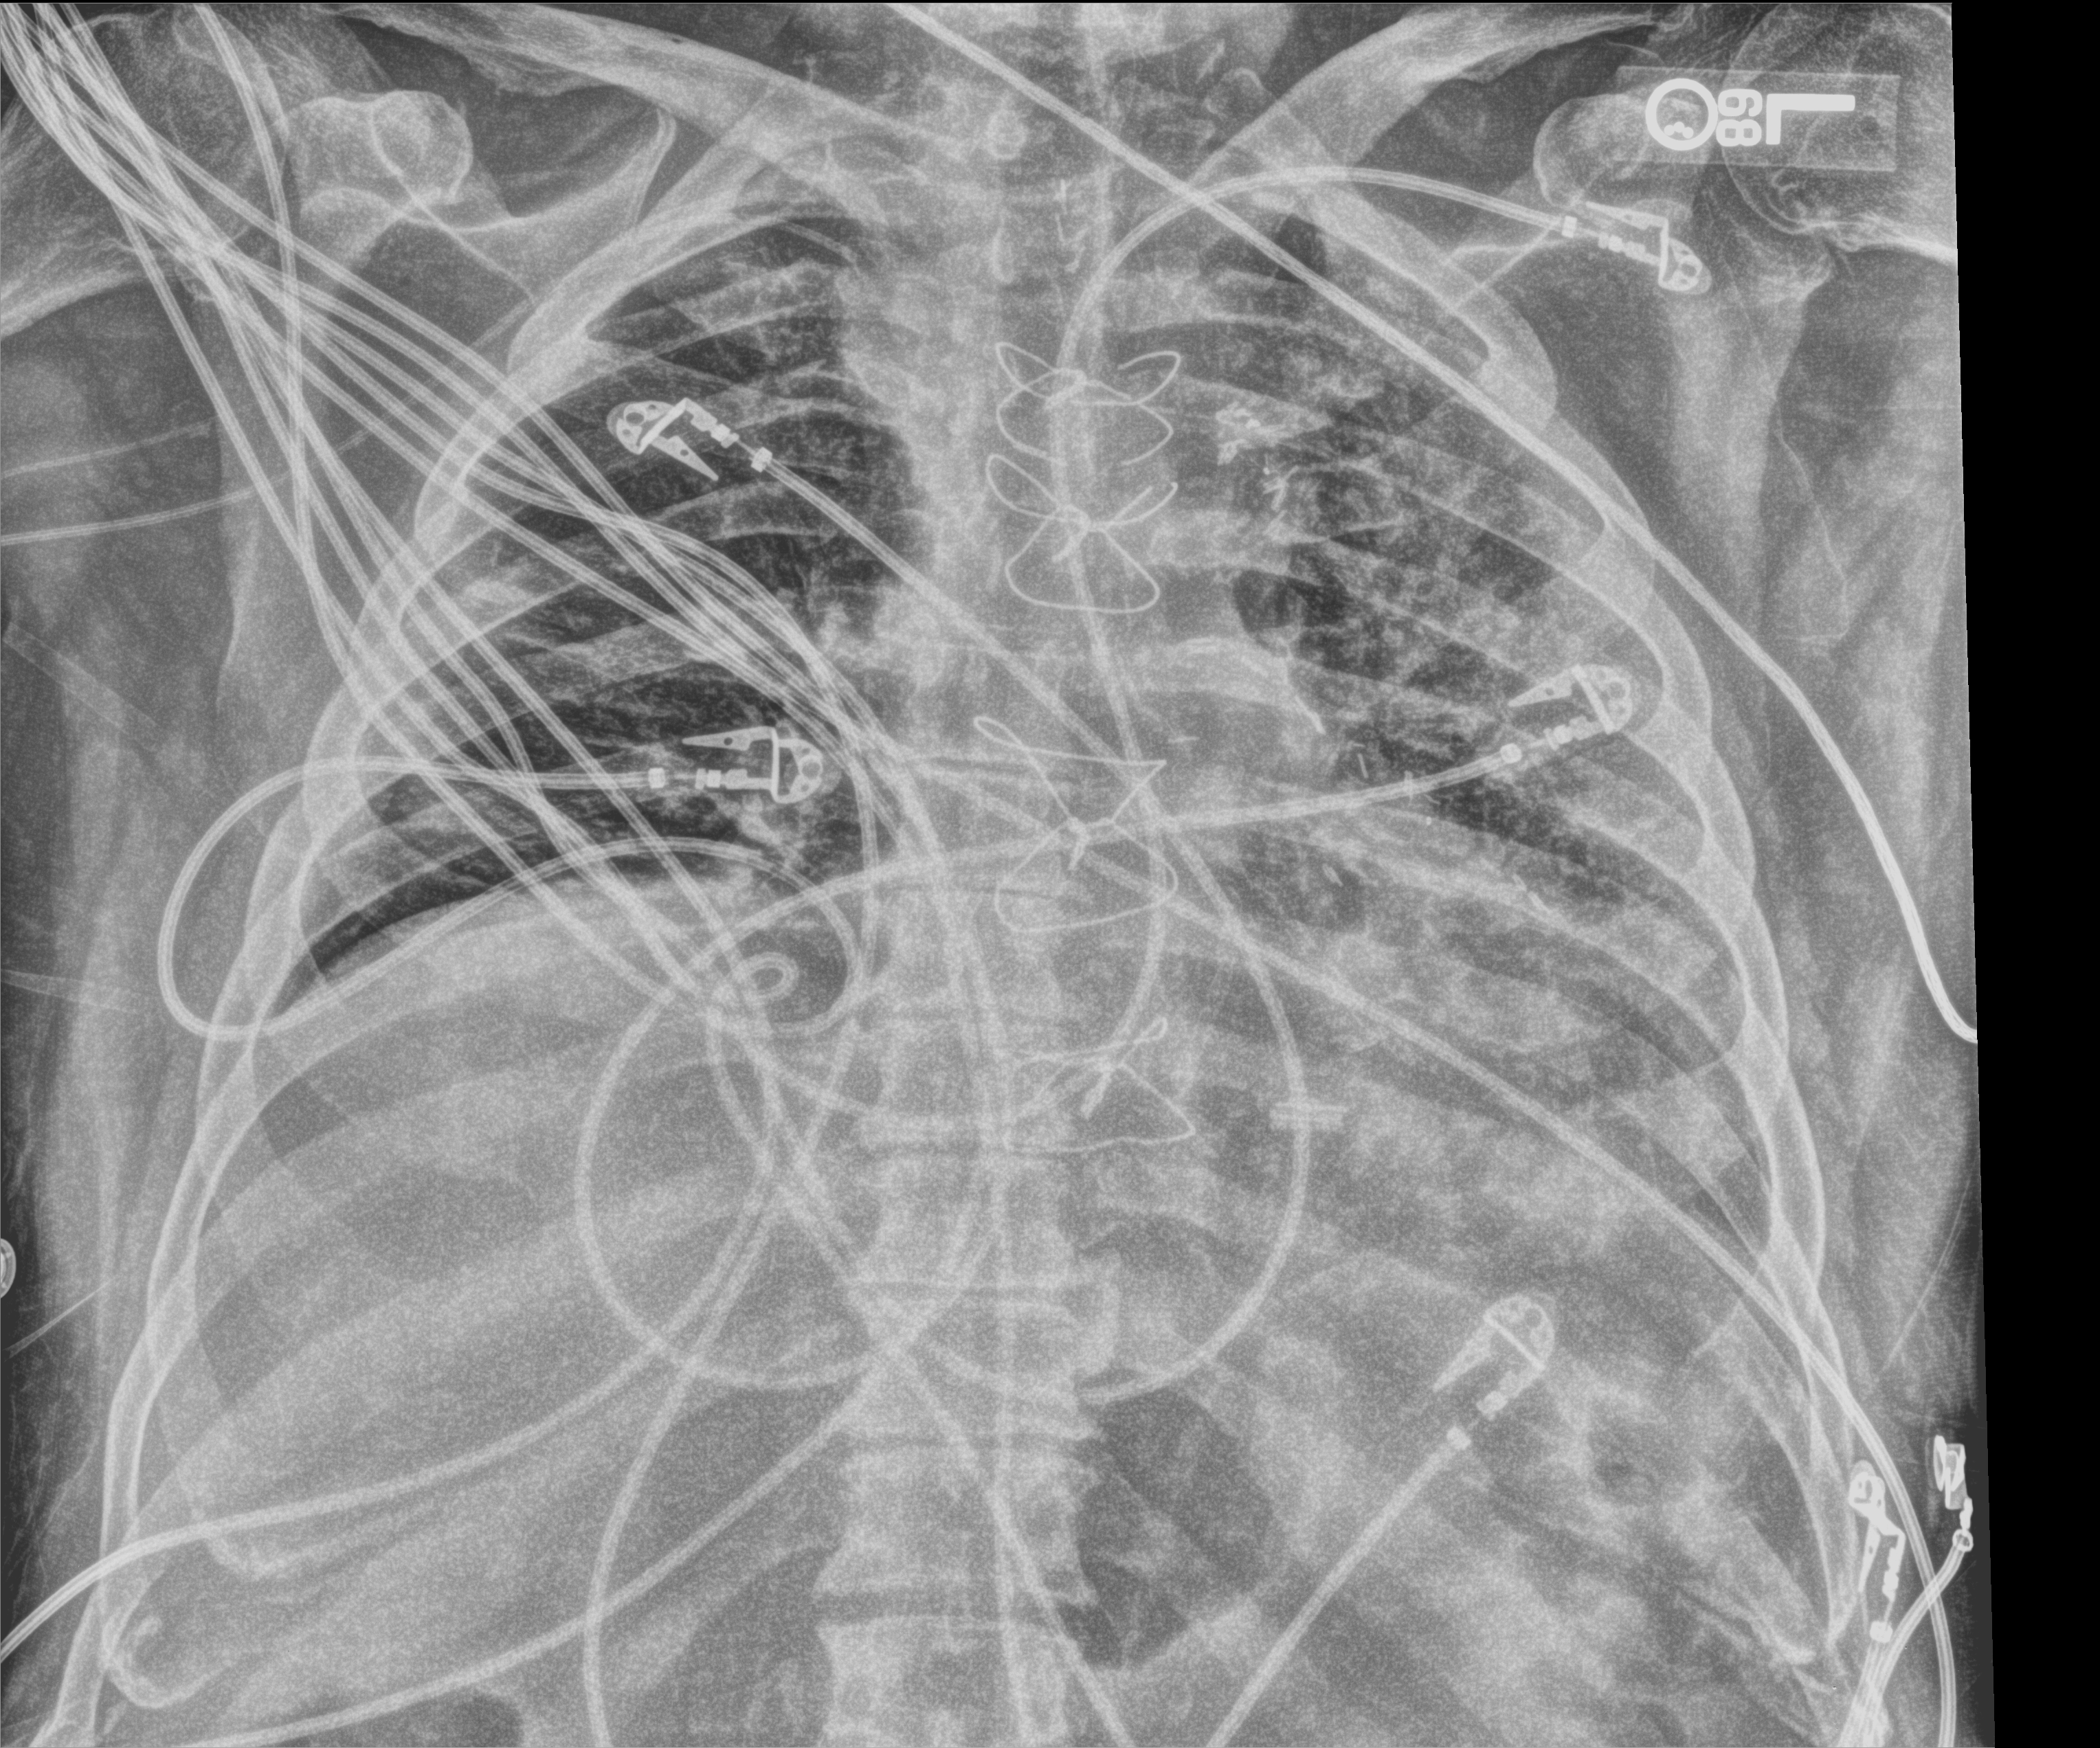
Bedside chest radiograph (computed radiography), anteroposterior (AP) projection. Male patient hospitalised with COVID-19, age 60–74 years.
From the hospital-stay record, not from the radiograph (when in the stay this image was taken is not recorded):
- other chronic lung disease (admission record): no
- smoking status (admission record): former
- chronic kidney disease (admission record): no